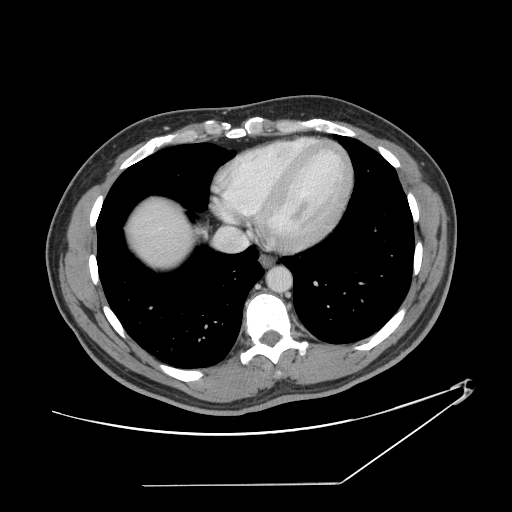
Contrast-enhanced abdominal CT, one axial slice. Slice 139 of 152 in the series (ordered by position). Soft-tissue window (W 400 / L 40 HU). 2.5 mm slice thickness. 512 × 512 image matrix. Male patient, age 45 years. From the clinical record (not read from this slice): diagnosis: colorectal cancer liver metastases, imaged before liver resection.
Annotated regions visible in this slice (expert manual segmentation):
- hepatic veins: box from (x=228, y=228) to (x=248, y=247) px
- liver: (x=131, y=199)–(x=190, y=266)
- planned liver remnant (the part of the liver to remain after resection): (x=131, y=198)–(x=190, y=266)